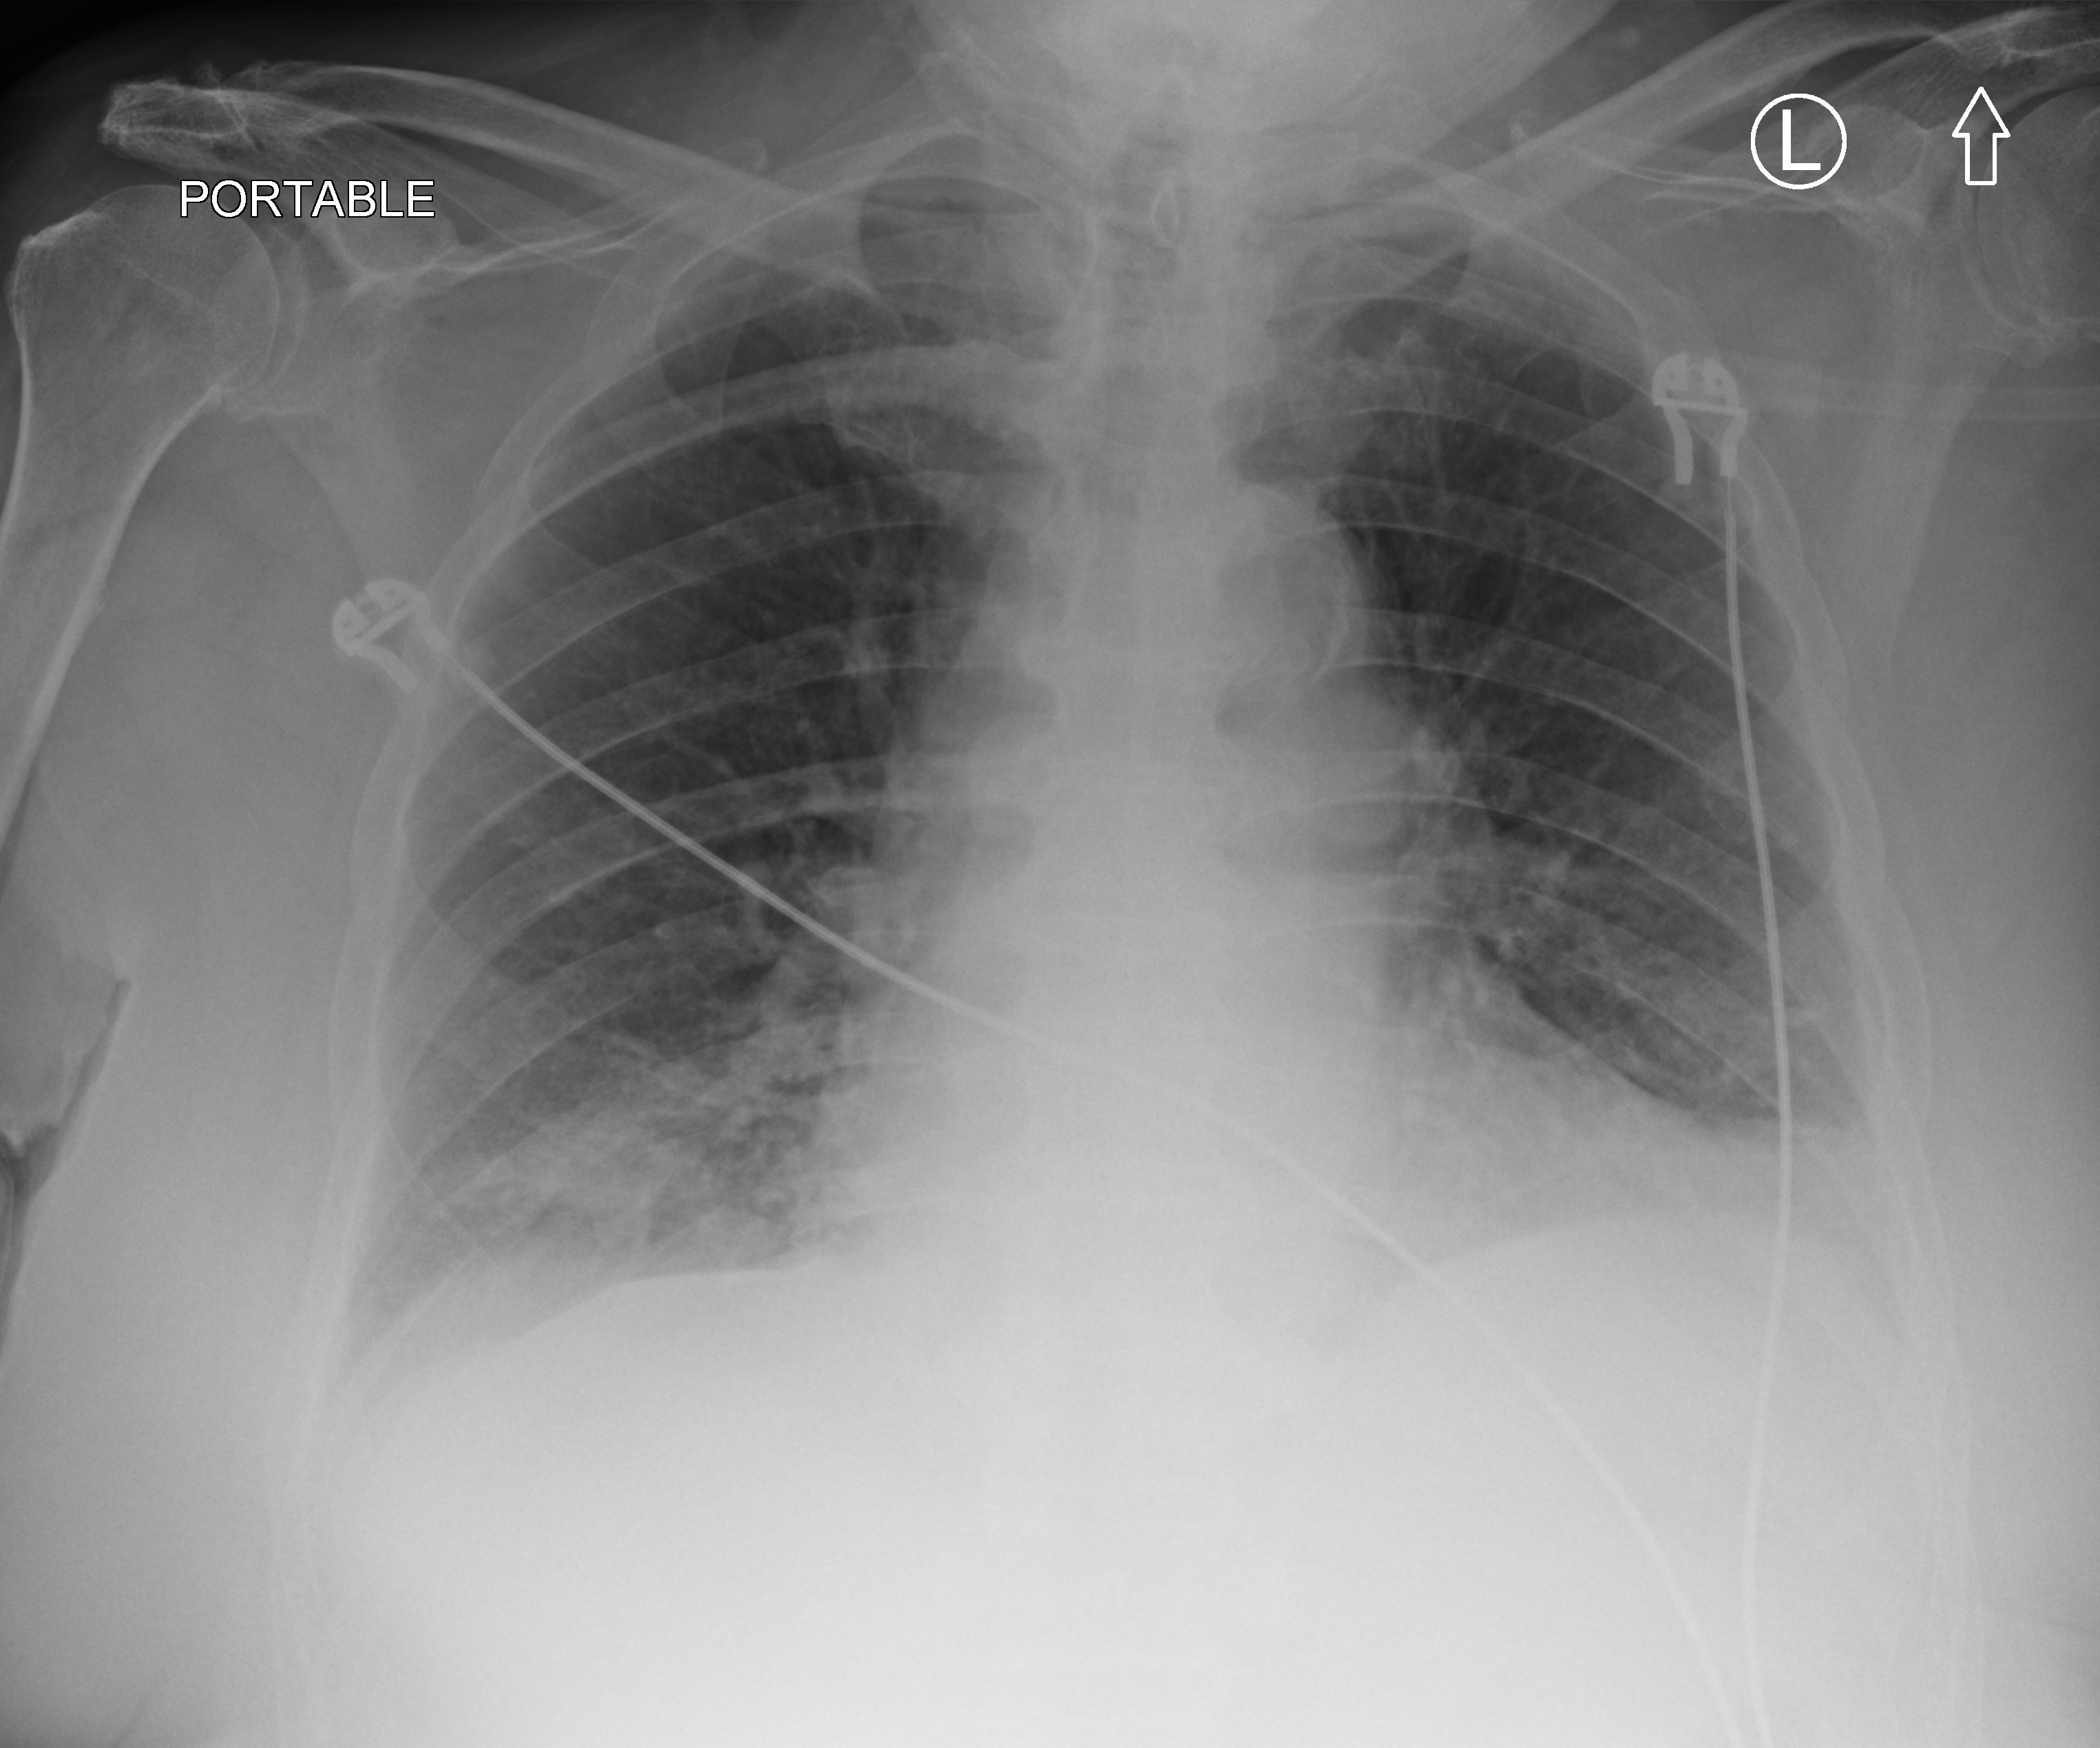
Portable chest radiograph, anteroposterior (AP) projection. Male patient hospitalised with COVID-19, age 75–90 years.
Admission-level facts for this patient (not findings on this image; timing relative to this image not recorded):
- admitted to intensive care during this hospital stay: no